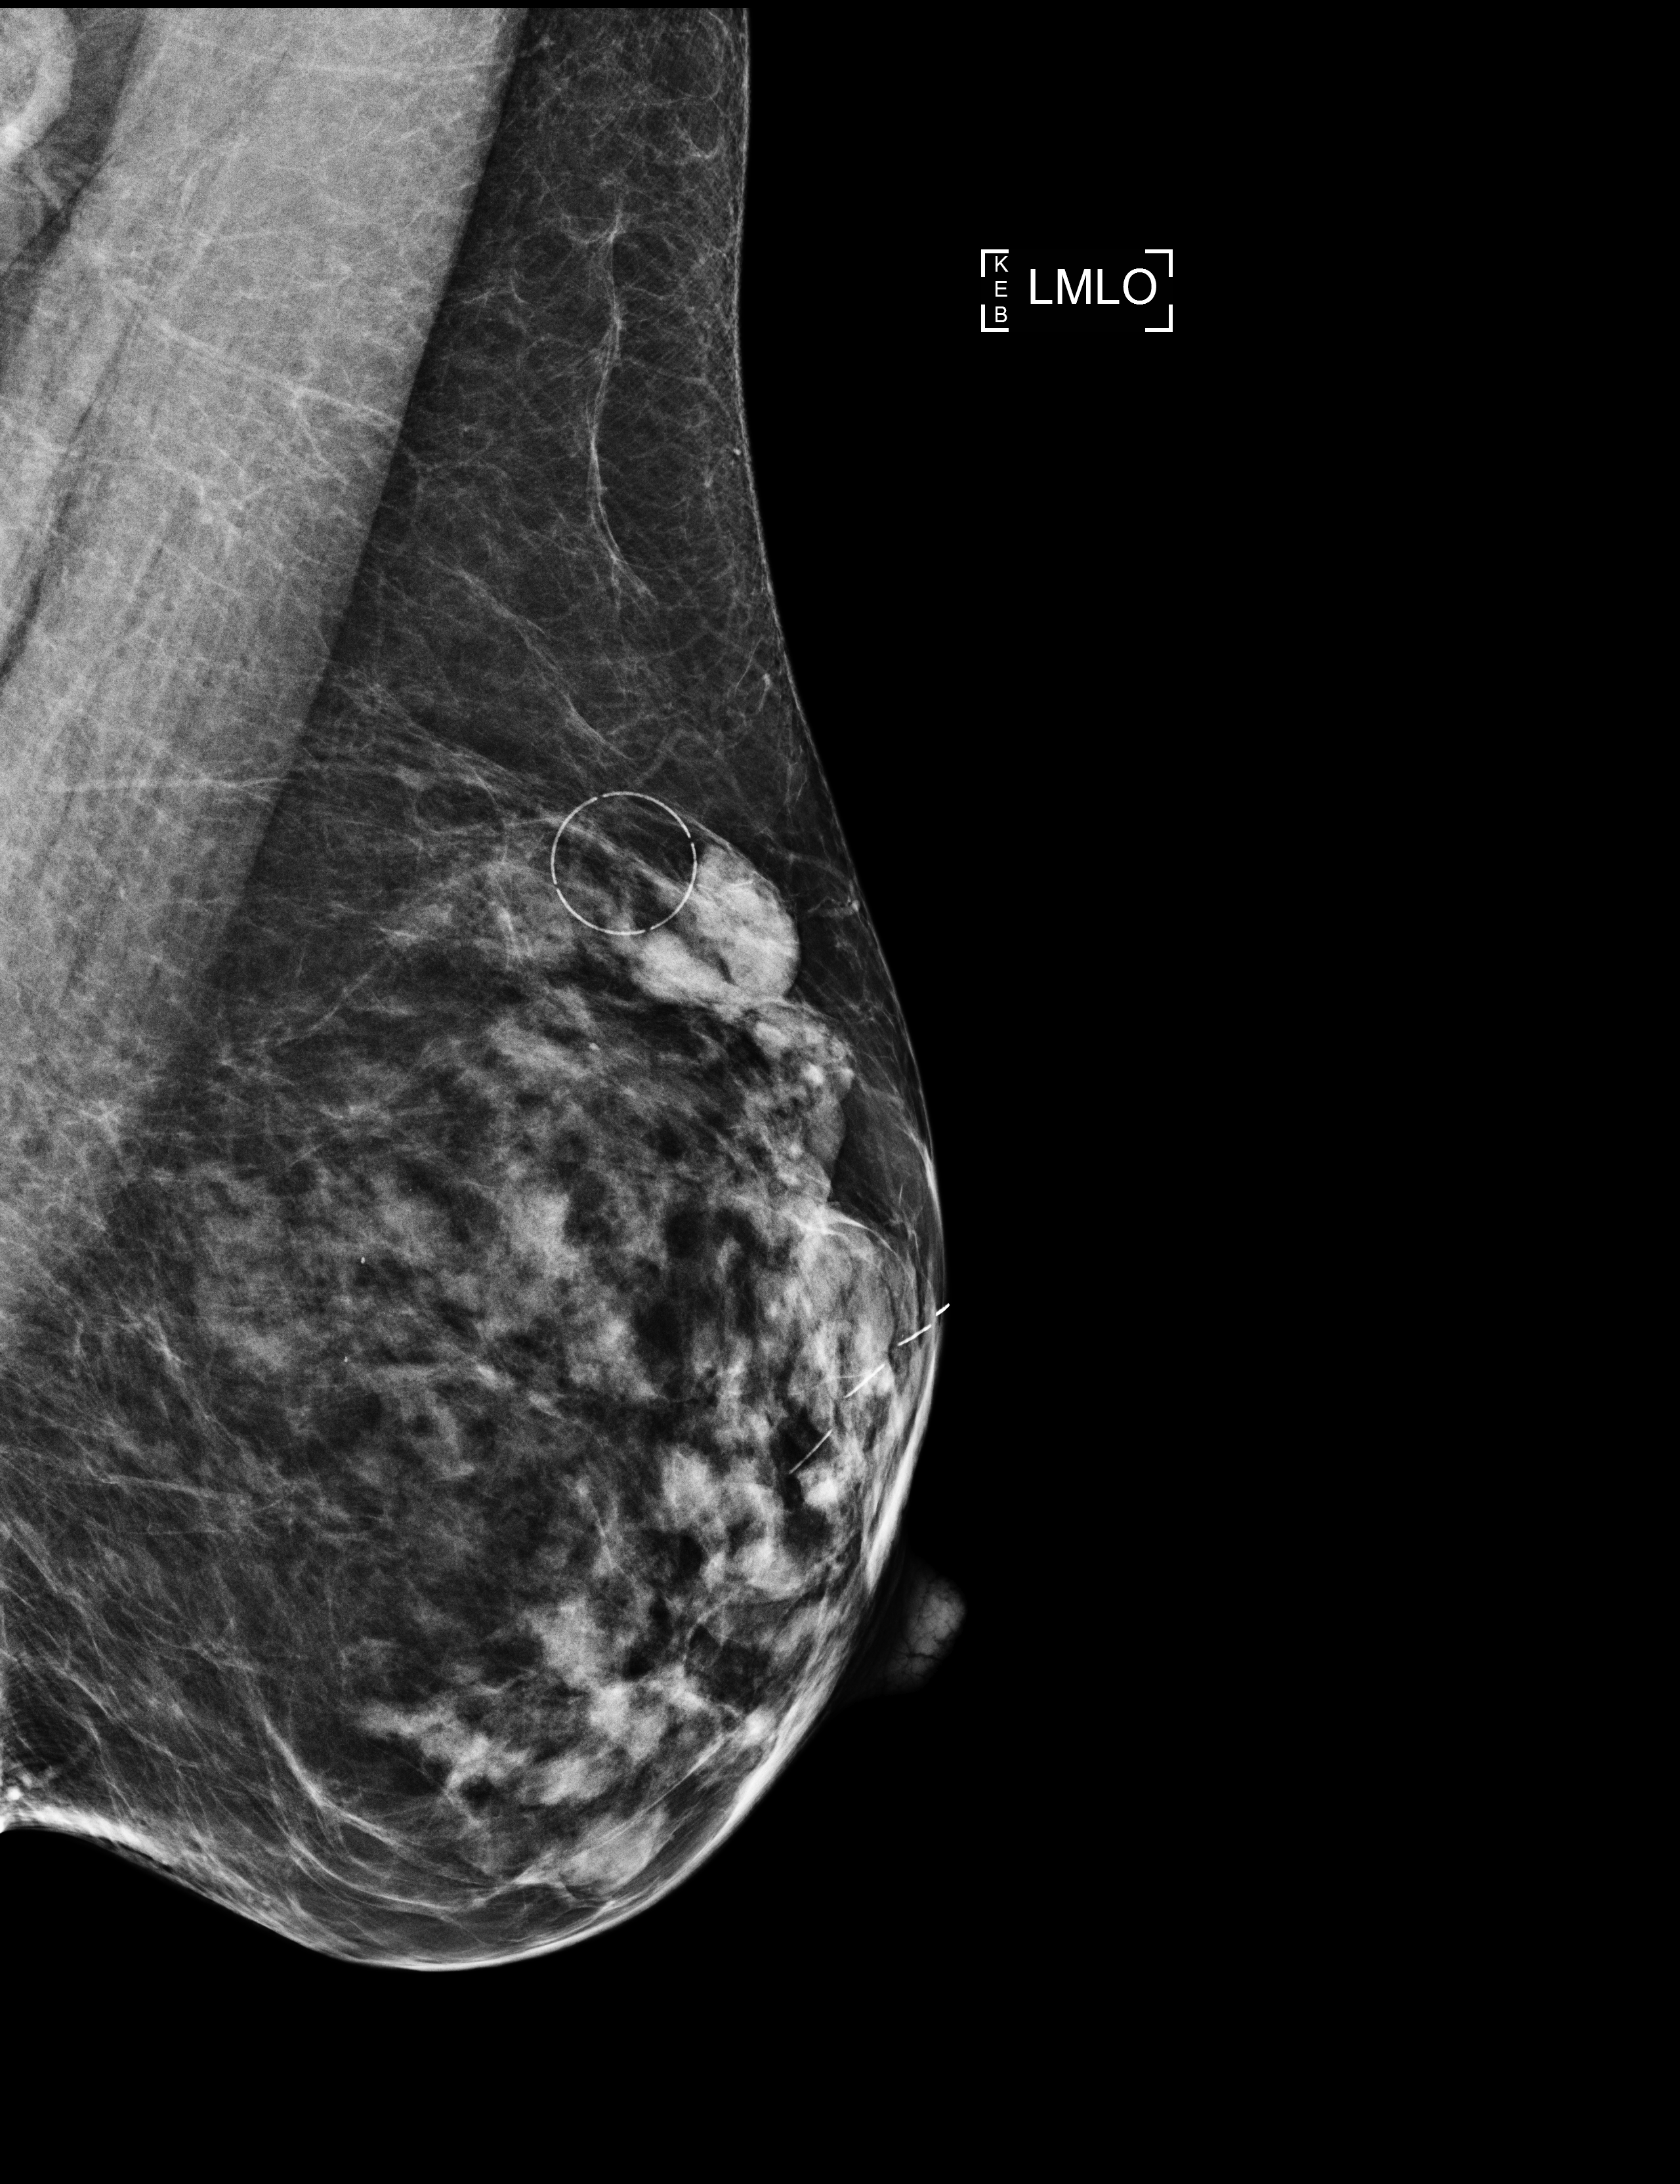
Full-field digital mammogram (FFDM), left breast, mediolateral oblique (MLO) view, annual screening mammography examination, compressed breast thickness 55 mm. Patient aged 72 years (female).
- breast density at the screening exam (both breasts): heterogeneously dense (BI-RADS density category c)
- final BI-RADS category for the screening round (tomosynthesis exam, both breasts): category 1
- recall: no recall after this screen